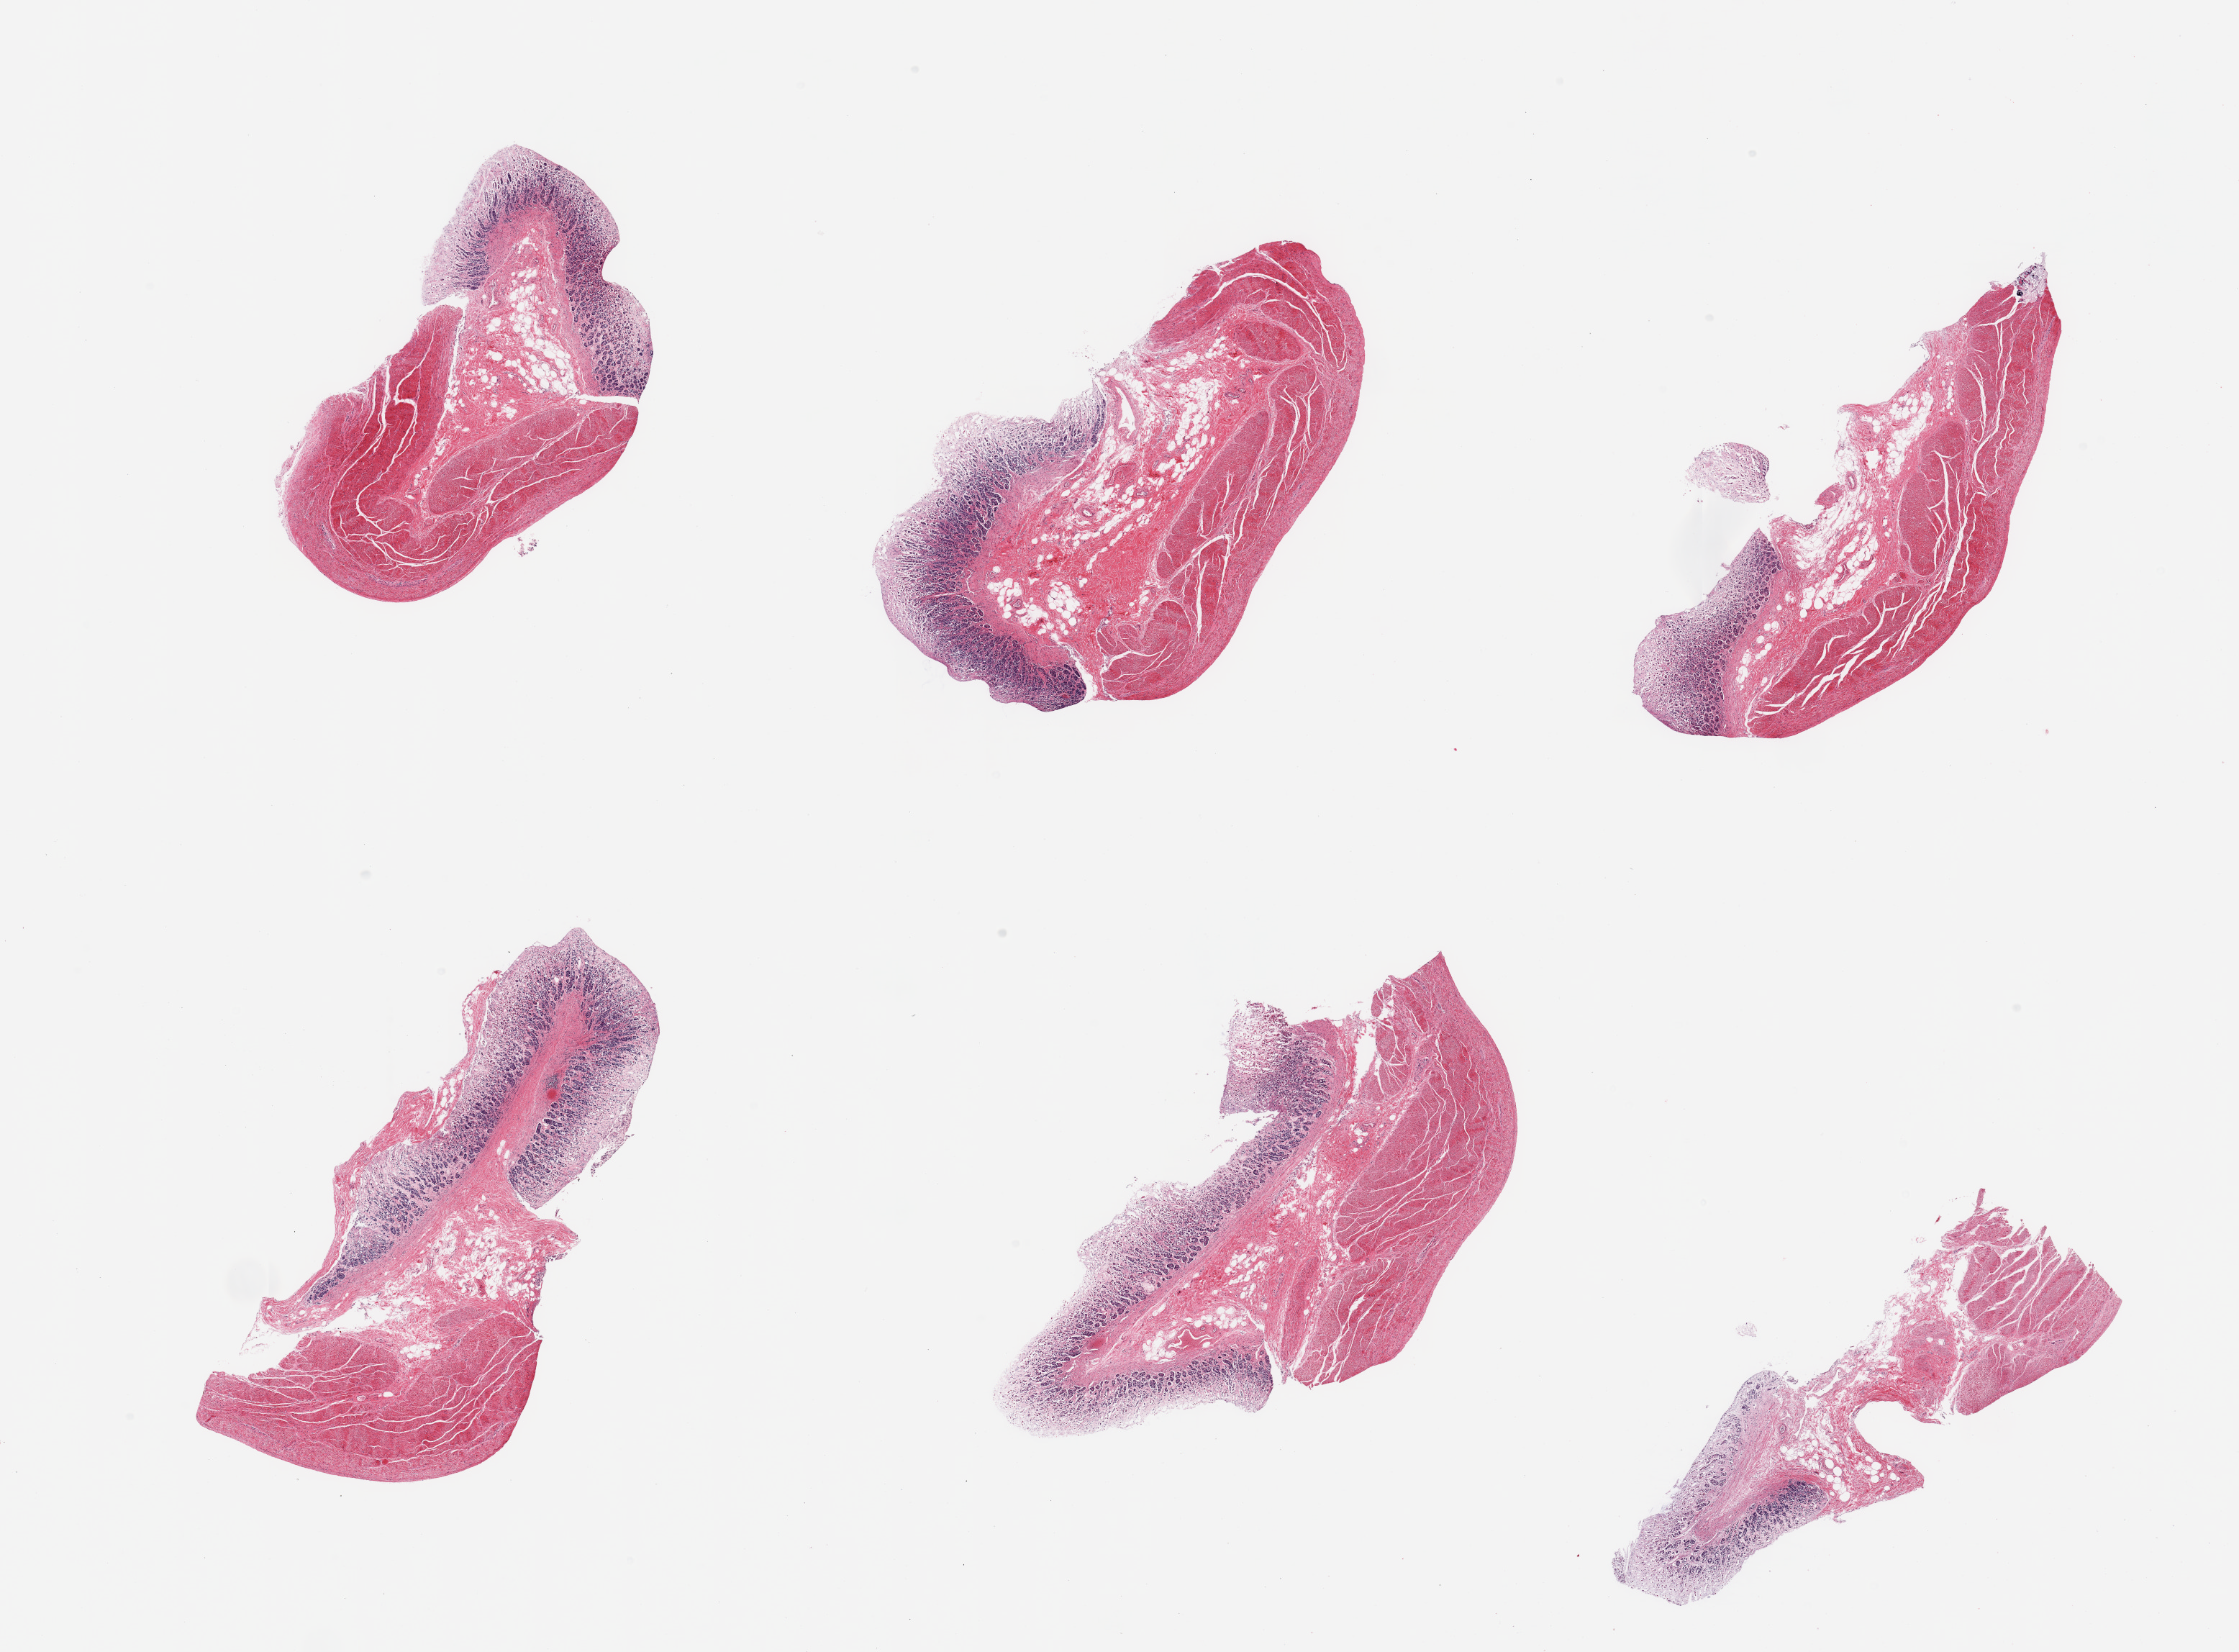
Haematoxylin and eosin whole-slide image, a low-resolution overview of the entire scanned area, about 24.6 x 18.2 mm (from a 20x scan). PAXgene-fixed, paraffin-embedded tissue. Section of stomach (target tissue). Donor tissue sample. Donor sex: male.
Reviewer comment on this tissue sample: 6 pieces; moderately to severely autolyzed gastric mucosa, muscularis is better preserved.